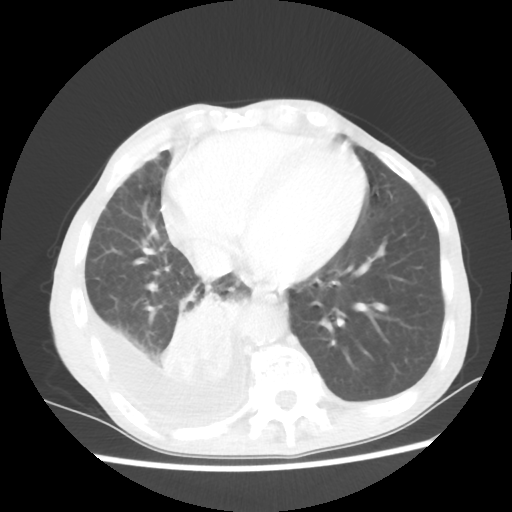
Chest CT, one axial slice. Position 20 of 60 along the scan axis. Reconstruction kernel STANDARD. 80 kVp. Lung window (W 1500 / L -600 HU). 512 × 512 image matrix. Male patient, age 76 years. Case-level facts recorded for this patient, not image findings: clinical TNM (as recorded): T3 N3 M1a; histopathological grade: G3.
Outlined on this slice (bounding box drawn by a radiologist):
- lung tumour (recorded histology: squamous cell carcinoma): bounding box (x1, y1, x2, y2) in pixels: (161, 286, 250, 391)